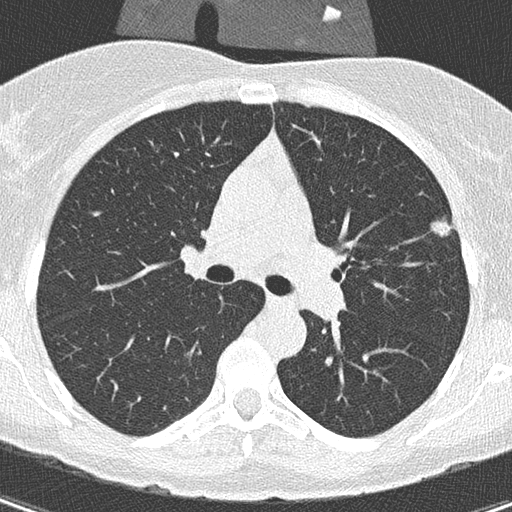
Chest CT (low-dose screening protocol), one axial image. Baseline annual screen. Lung window (W 1500 / L -600 HU). 2 mm slice thickness. Lung (sharp) reconstruction kernel (B50f). 120 kVp. Slice 110 of 305 in the series. Female, age 56 years at enrolment.
Expert-annotated lung lesion, bounding box [x1, y1, x2, y2] px = [421, 192, 468, 245]. Reader record for this screening exam (exam-level; its link to the box is not recorded): non-calcified nodule or mass ≥4 mm, left upper lobe, 110 × 106 mm, spiculated (stellate) margins, soft tissue attenuation. Official screen result: positive, change unspecified: nodule(s) >= 4 mm or enlarging nodule(s), mass(es), or other non-specific abnormalities suspicious for lung cancer.